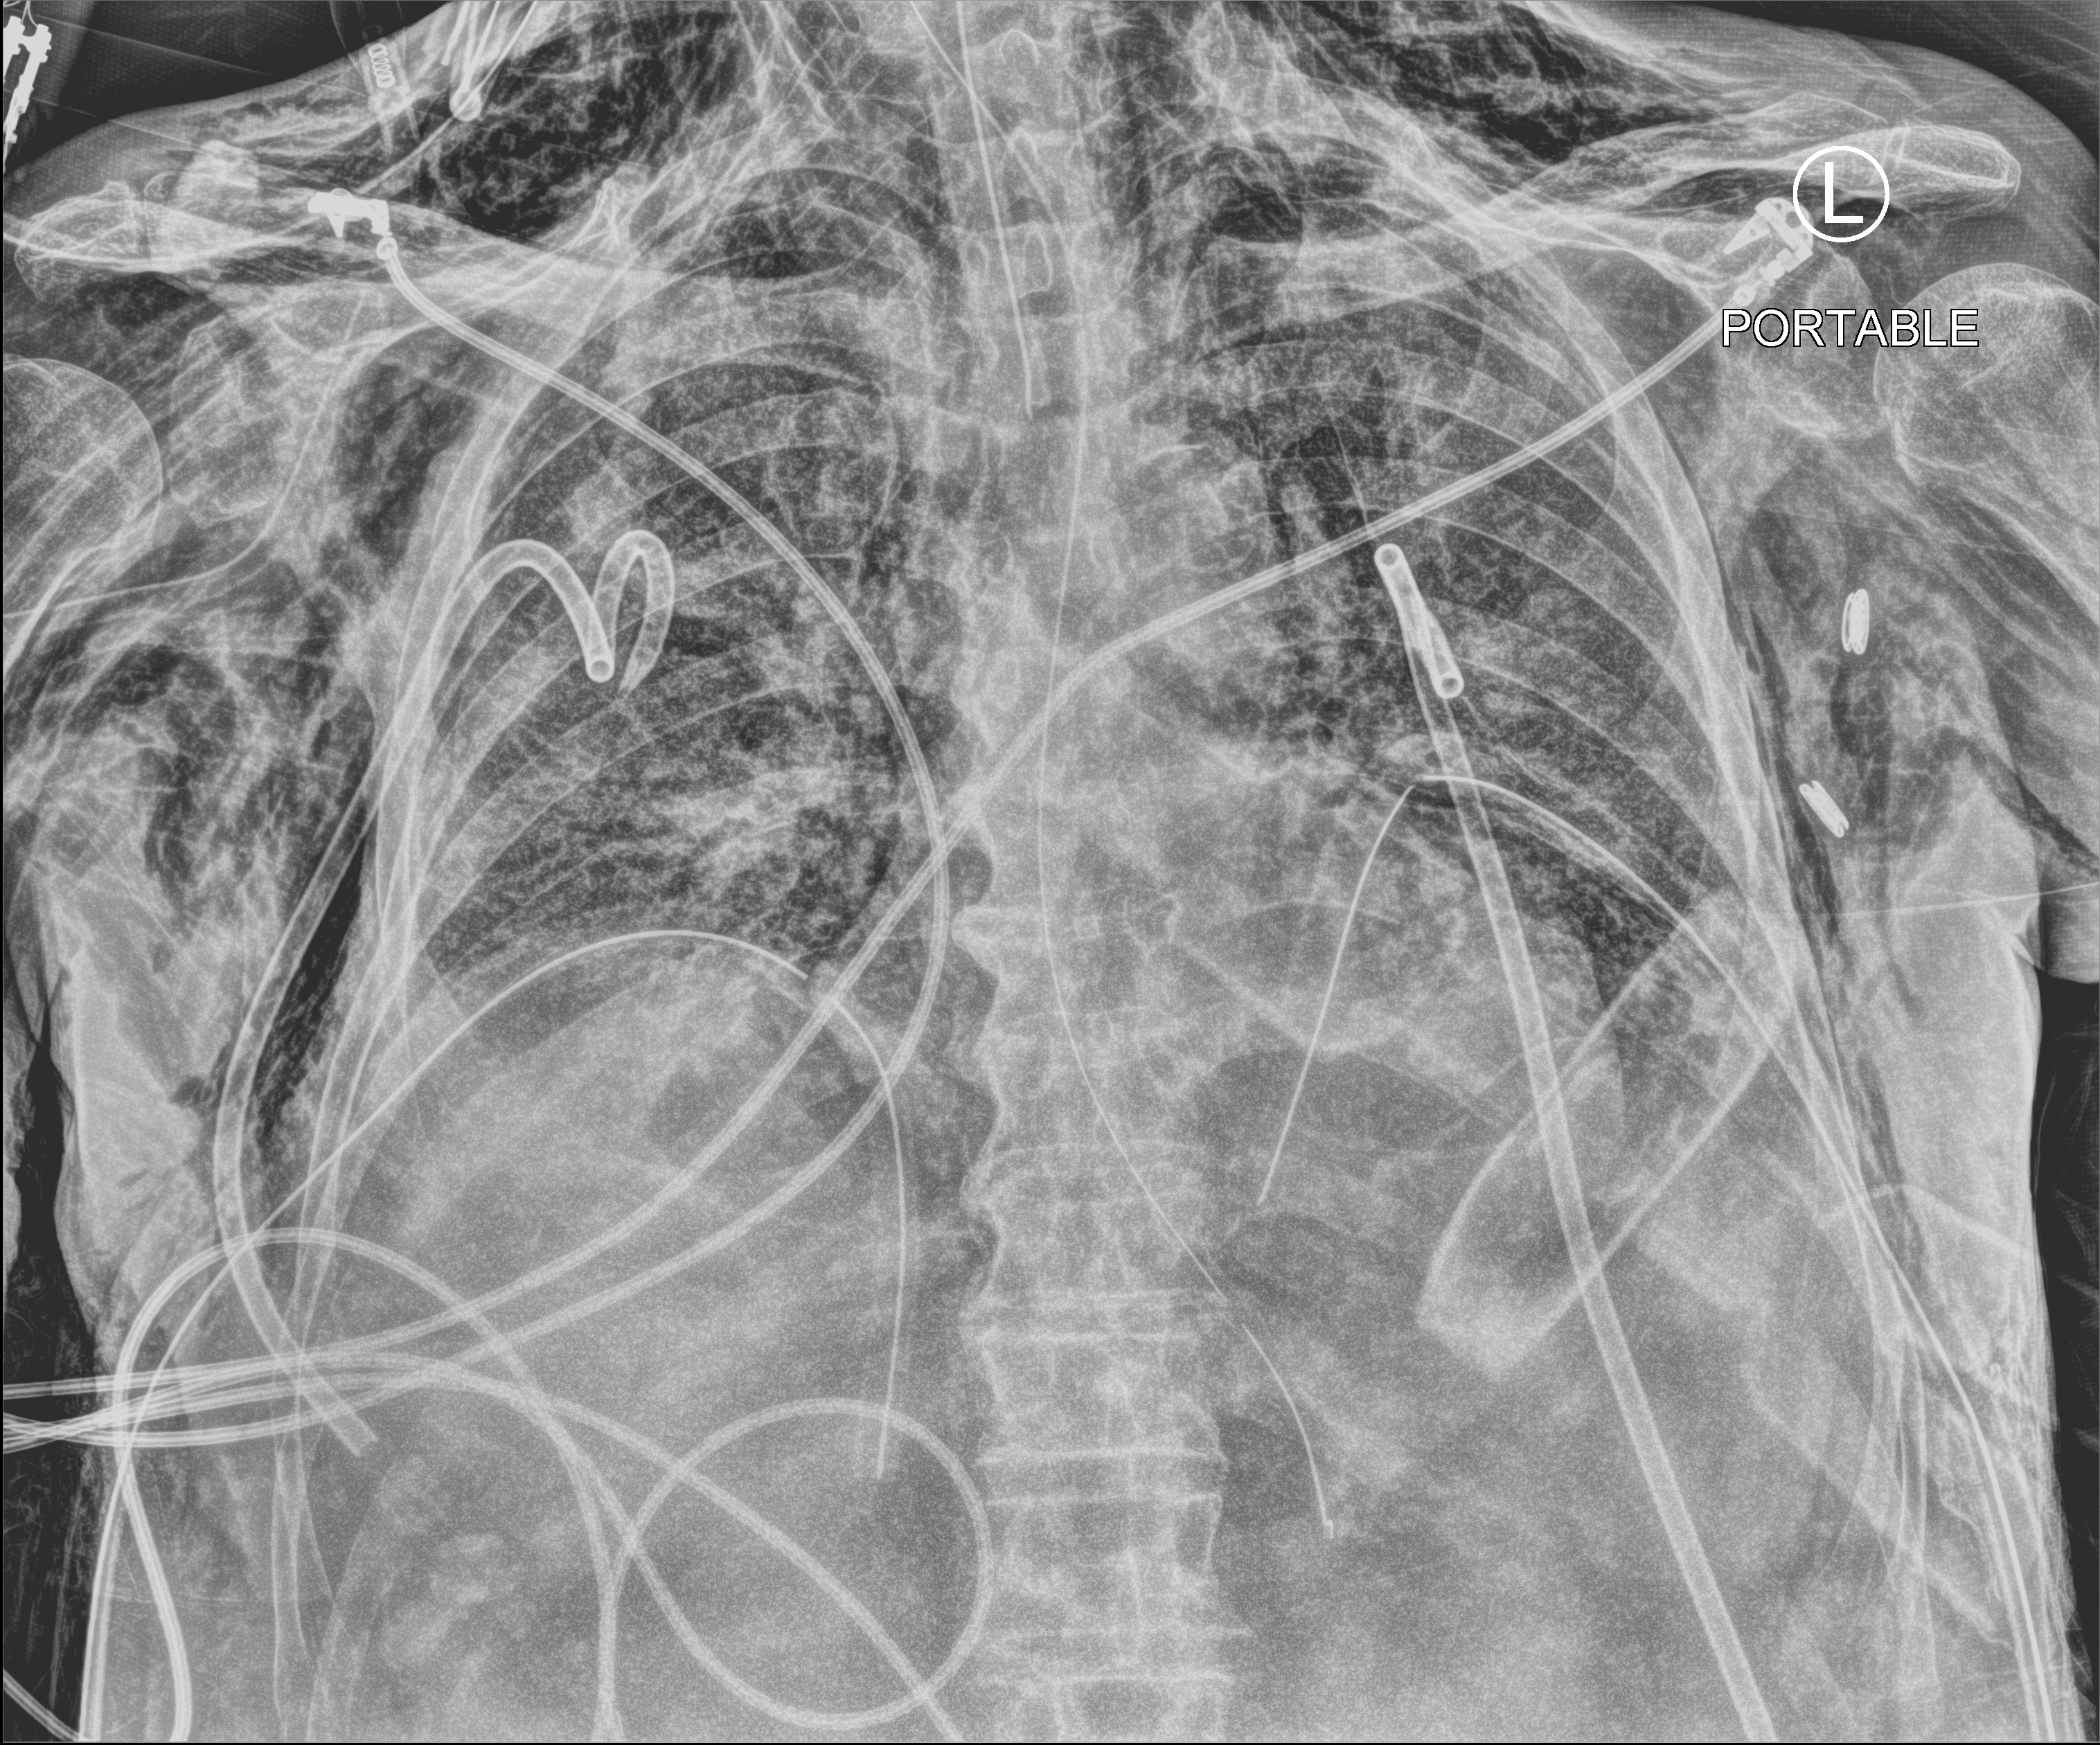
Portable chest radiograph; anteroposterior (AP) projection. Patient hospitalised with COVID-19; male, aged 75–90 years.
Admission-level facts for this patient (not findings on this image; timing relative to this image not recorded): mechanically ventilated during this hospital stay: yes.